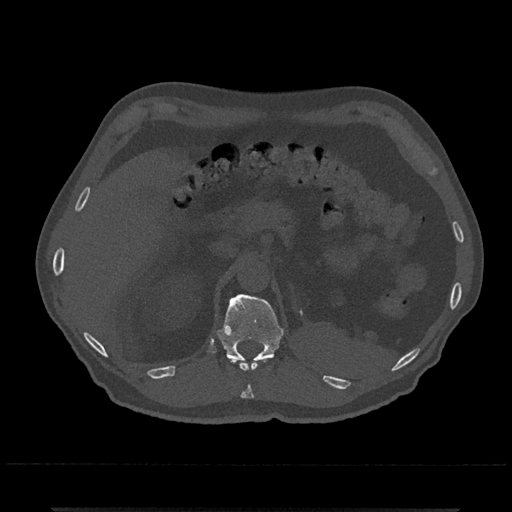
CT including the spine, one axial slice. Position 449 of 797 along the scan axis. Reconstruction kernel Br40s/3. 120 kVp. Bone window (W 1800 / L 400 HU). 512 × 512 image matrix, field of view 393 × 393 mm. Patient: male, 67 years. From the clinical record (not read from this slice): primary cancer: prostate.
Annotated regions visible in this slice (semi-automatically segmented with operator editing):
- T11 vertebra: bounding box (x1, y1, x2, y2) in pixels: (229, 358, 266, 399)
- T12 vertebra: (216, 294, 284, 363)